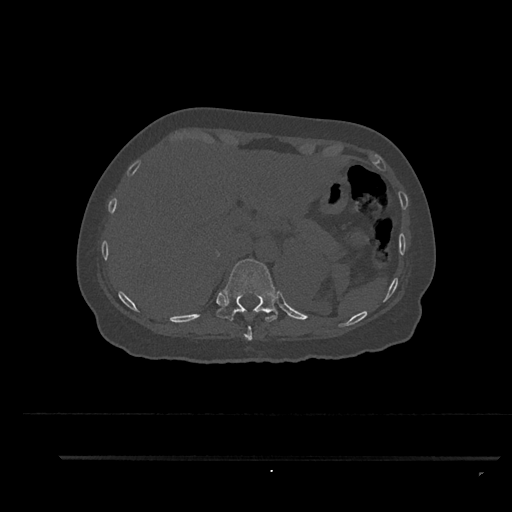
CT including the spine, one axial slice; position 328 of 797 along the scan axis; reconstruction kernel Br40s/3; 120 kVp; bone window (W 1800 / L 400 HU); 512 × 512 image matrix, field of view 408 × 408 mm. Patient: female, 44 years. From the clinical record (not read from this slice): primary cancer: renal; vertebrae with lytic lesions (as recorded): L1.
Outlined on this slice (semi-automatically segmented with operator editing):
- T10 vertebra: bounding box <244,311,253,340> (left, top, right, bottom; pixels)
- T11 vertebra: <216,259,278,322>